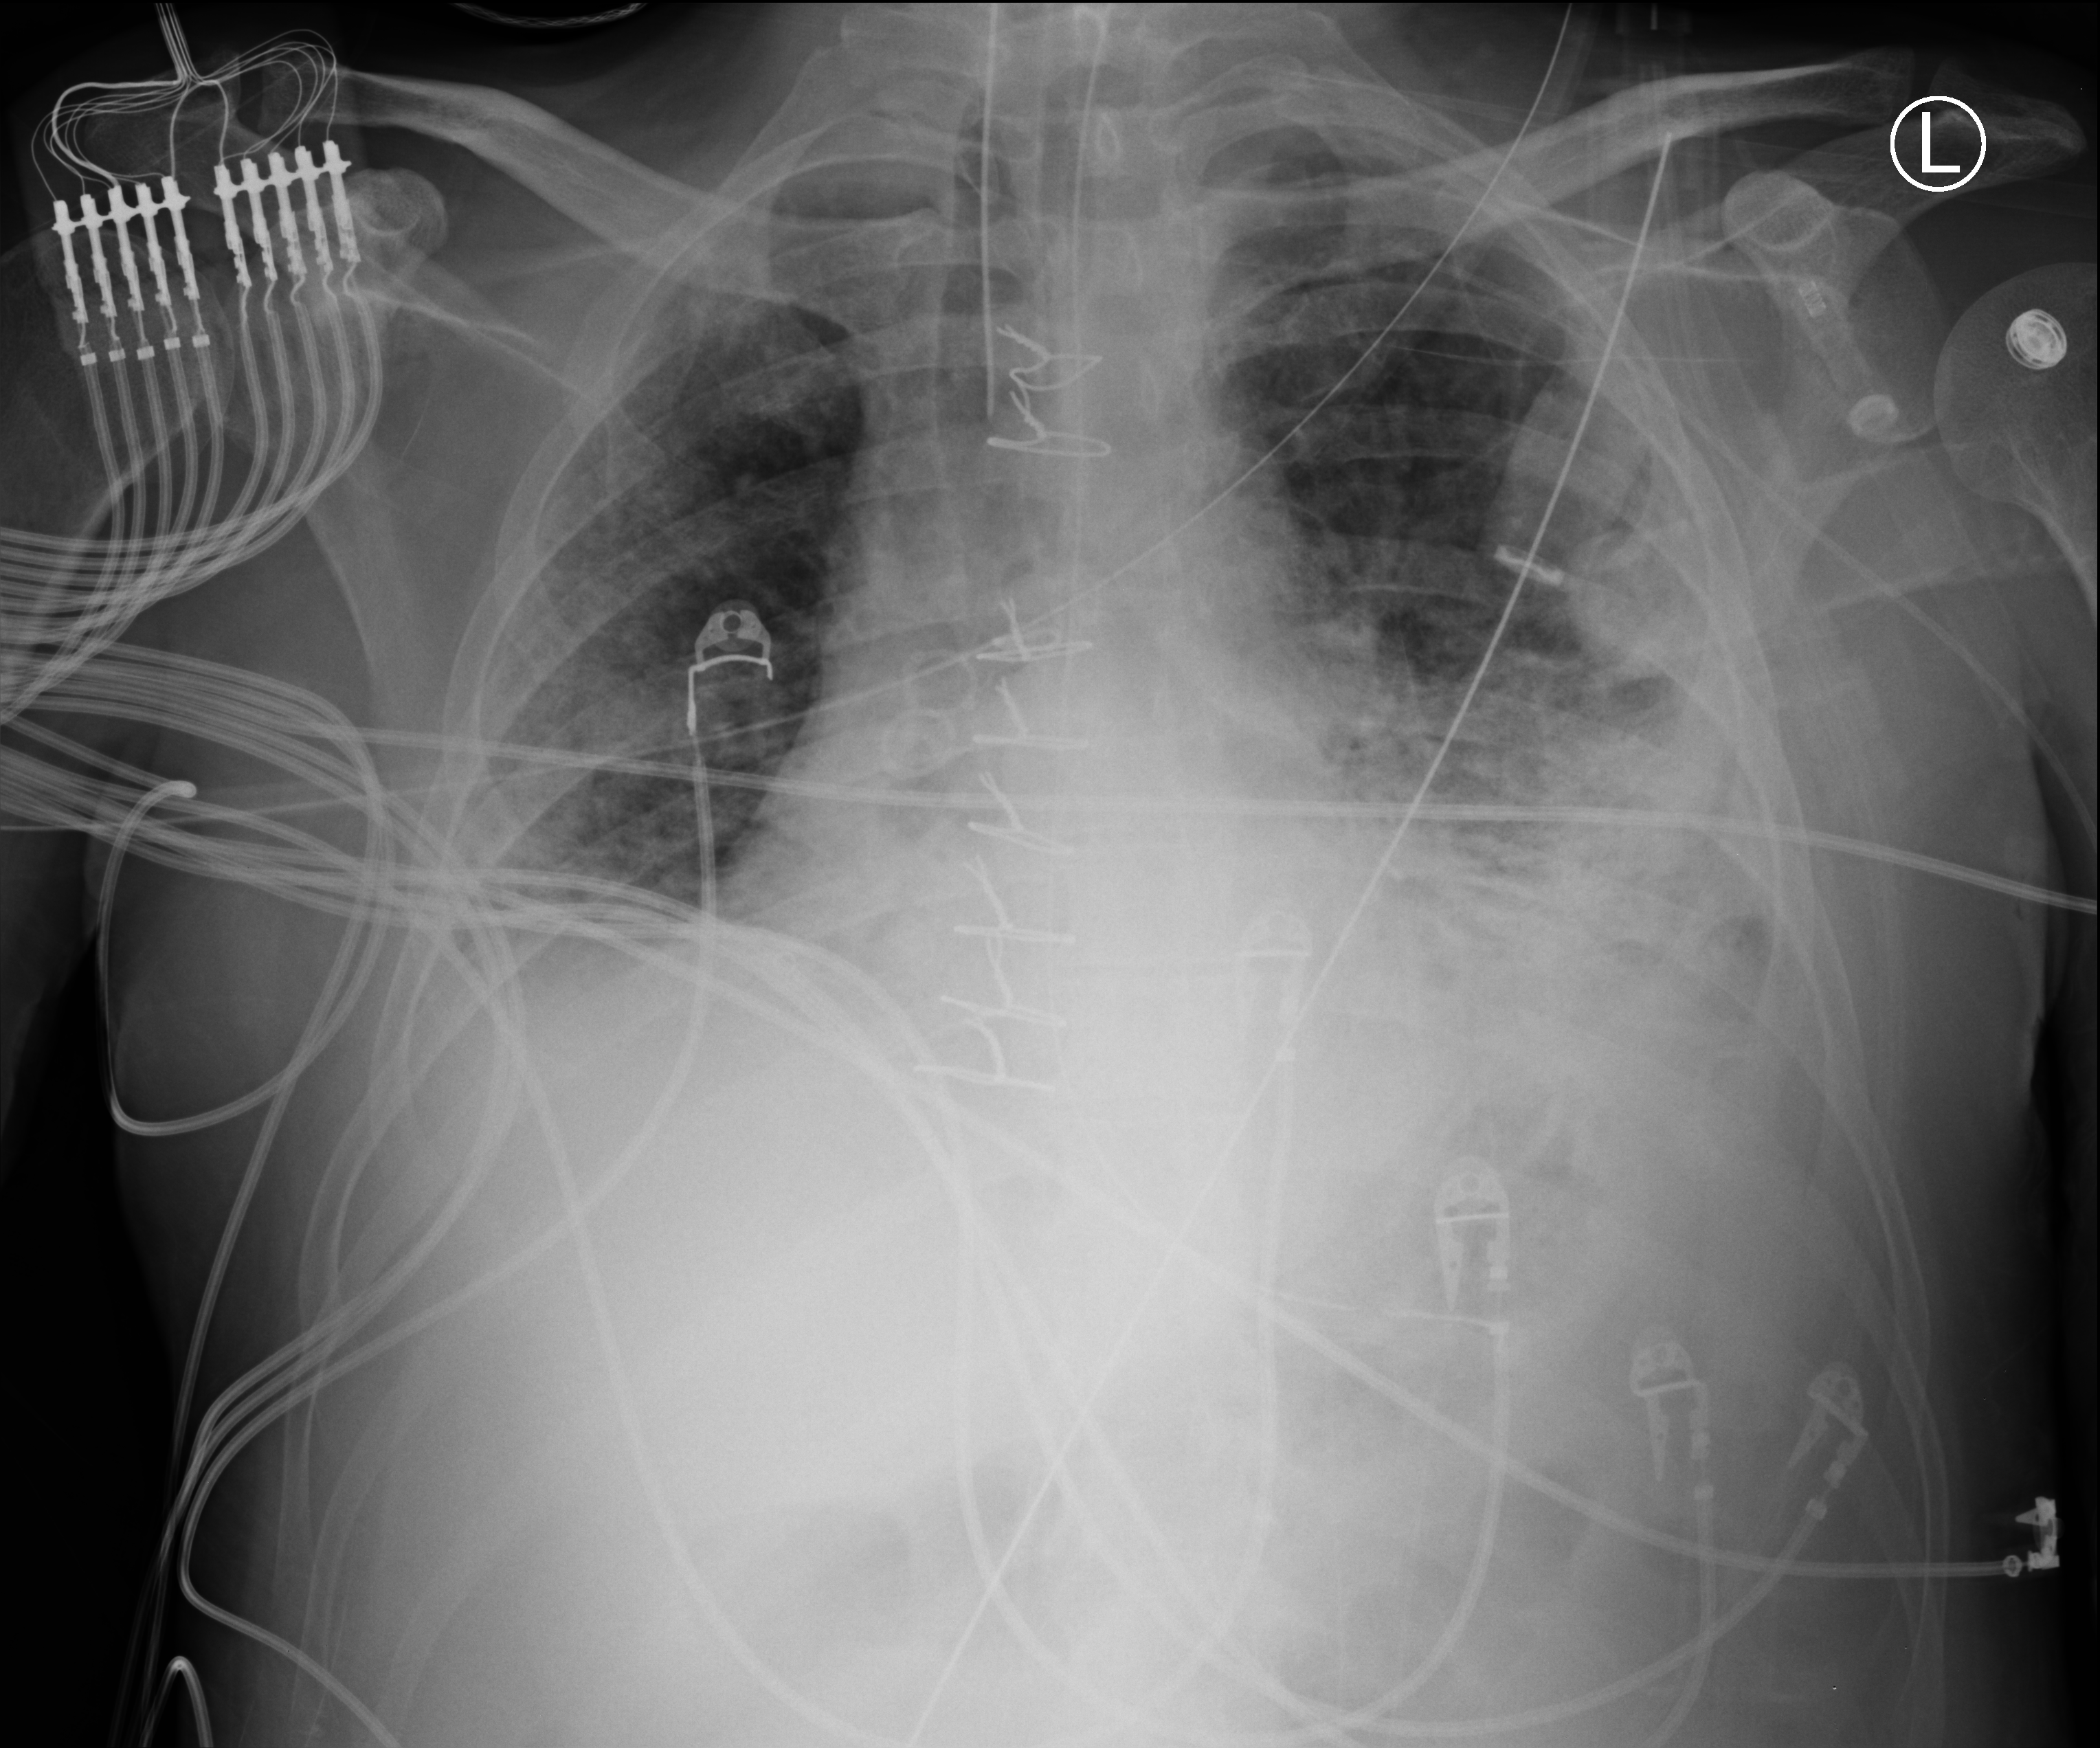
Portable chest radiograph; anteroposterior (AP) projection. Male patient hospitalised with COVID-19, age 18–59 years.
From the hospital-stay record, not from the radiograph (when in the stay this image was taken is not recorded): mechanically ventilated during this hospital stay: yes.